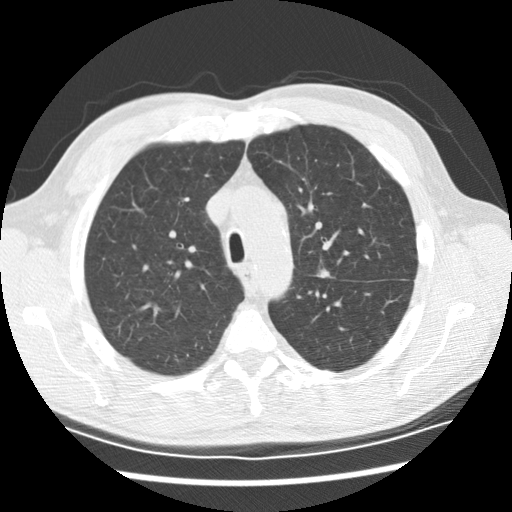
Low-dose screening chest CT, one axial slice; slice 150 of 208 in the series (ordered by position); reconstruction kernel STANDARD; 120 kVp; lung window (W 1500 / L -600 HU); 2.5 mm slice thickness; 512 × 512 image matrix, field of view 340 × 340 mm.
Outlined on this slice (outlined manually by an expert reader):
- lesion 1 (tumor, upper lobe of left lung): box from (x=316, y=269) to (x=330, y=278) px